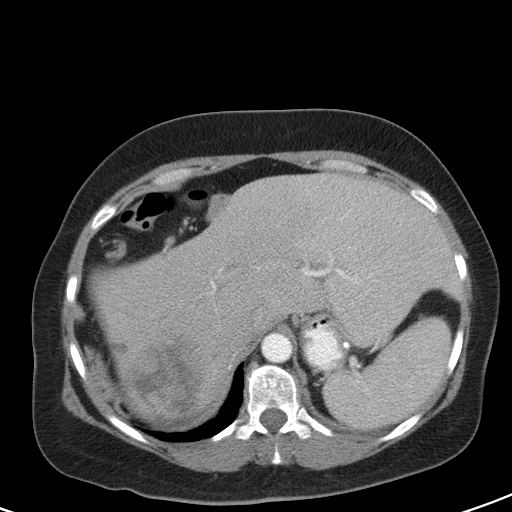
Contrast-enhanced abdominal CT, one axial slice; slice 79 of 126 in the series (ordered by position); intravenous contrast given; soft-tissue window (W 400 / L 40 HU); 5 mm slice thickness; 512 × 512 image matrix. Patient: female, 51 years. Case-level facts recorded for this patient, not image findings: diagnosis: adrenocortical carcinoma; tumour side: right adrenal; tumour size at pathology: 17 cm; Ki-67 index: 12 %; stage (as recorded): 2.
Outlined on this slice (semi-automatic segmentation, software-assisted and operator-edited):
- mass: bounding box (x1, y1, x2, y2) in pixels: (130, 340, 204, 420)